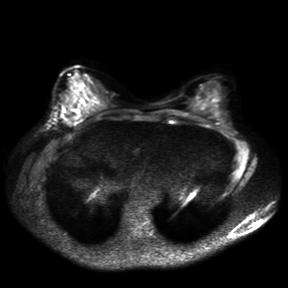
Breast MRI, one axial slice. Slice 17 of 30 in the series (ordered by position). Diffusion-weighted series; image 2 of 4 stored at this slice position (different b-values; order by instance number). 3 T. 4 mm slice thickness. 288 × 288 image matrix, field of view 360 × 360 mm. Female patient.
Structures marked on this image (outlined manually by an expert reader):
- tumour on diffusion-weighted imaging: bounding box [x1, y1, x2, y2] px = [59, 111, 80, 125]